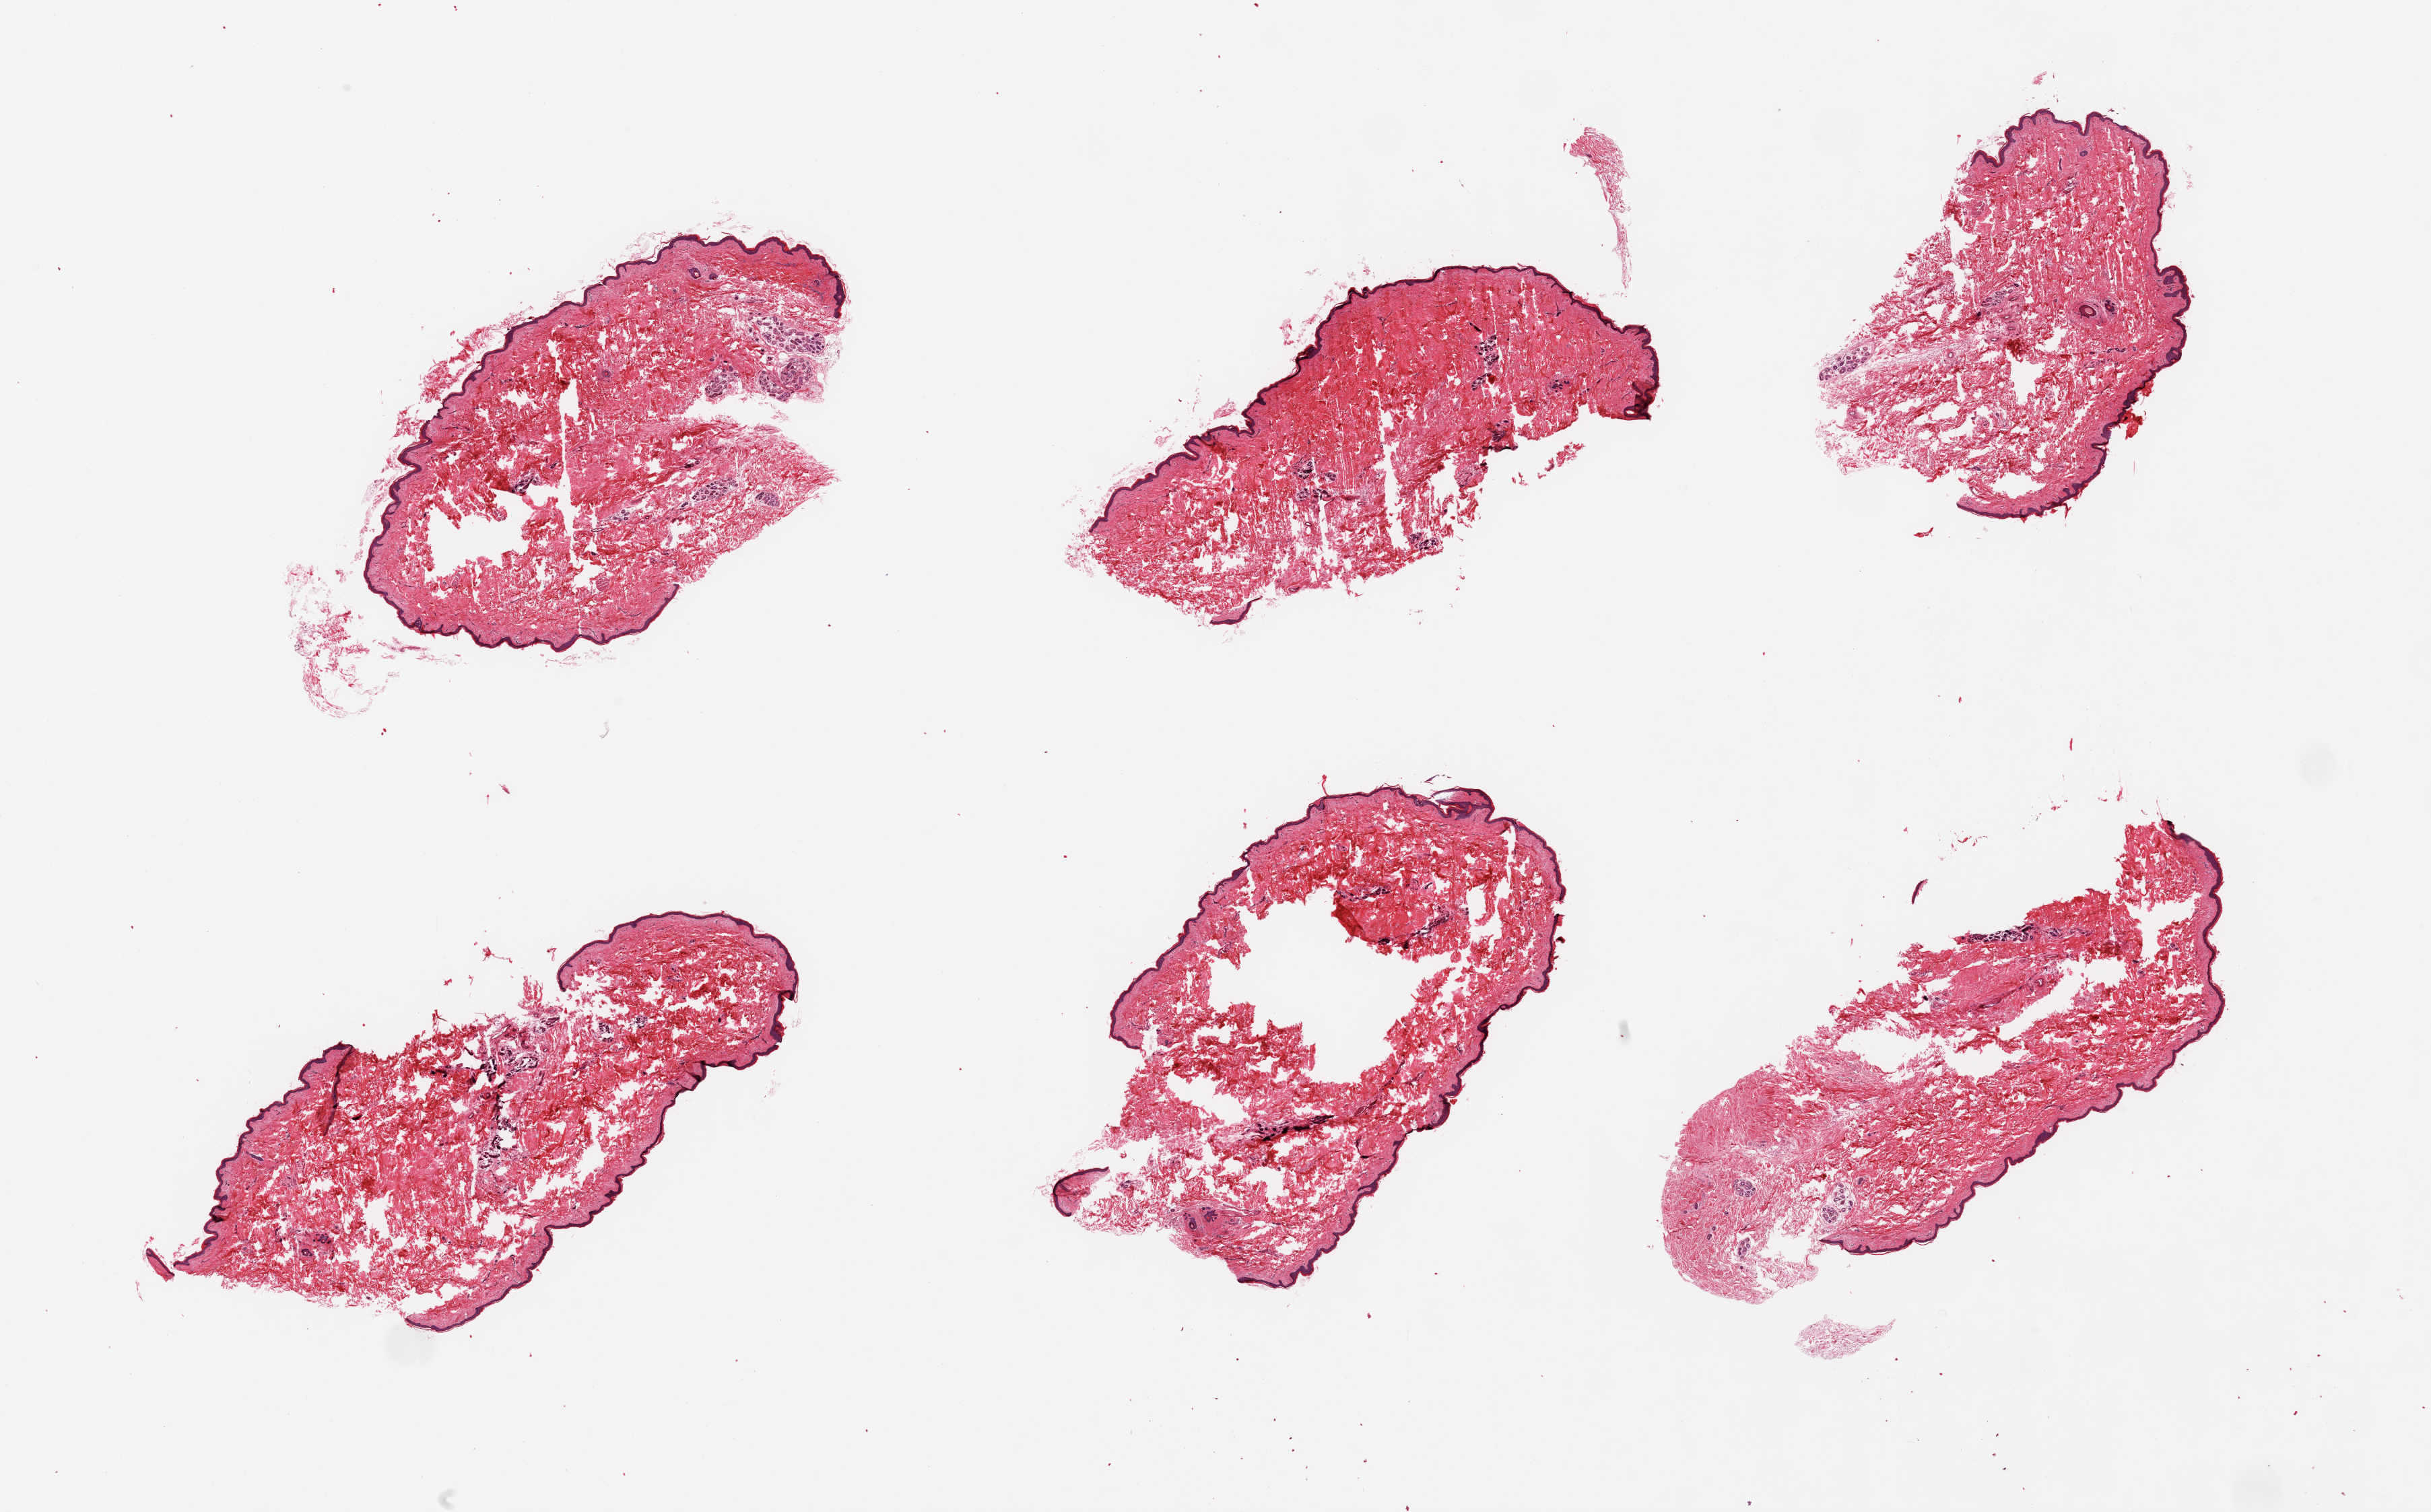
Whole-slide image, H&E stain — shown as a low-resolution overview of the whole scanned area (about 28.5 x 17.8 mm, from a 20x scan), PAXgene-fixed, paraffin-embedded tissue, section of skin of suprapubic region (target tissue), donor tissue sample. Donor: male.
Pathologist's review note for this sample: 6 pieces, no dermal fat; squamous epithelium is ~30-35 microns.